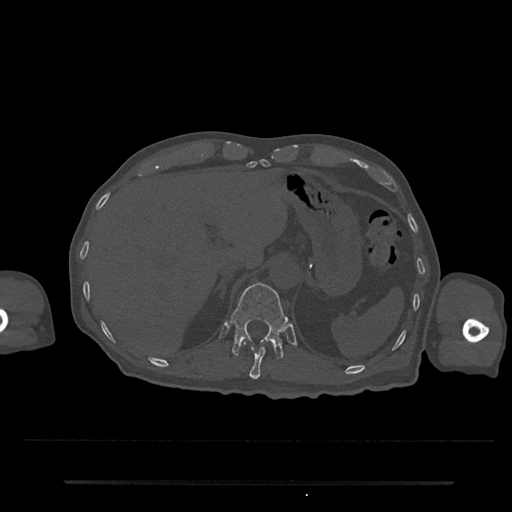
CT including the spine, one axial slice. Slice 218 of 797 in the series (ordered by position). Reconstruction kernel Br40s/3. 120 kVp. Bone window (W 1800 / L 400 HU). 0.5 mm slice thickness. 512 × 512 image matrix, field of view 427 × 427 mm. Male patient, age 74 years. From the clinical record (not read from this slice): primary cancer: prostate.
Outlined on this slice (semi-automatically segmented with operator editing):
- T11 vertebra: bounding box <242,341,273,380> (left, top, right, bottom; pixels)
- T12 vertebra: <231,283,288,359>